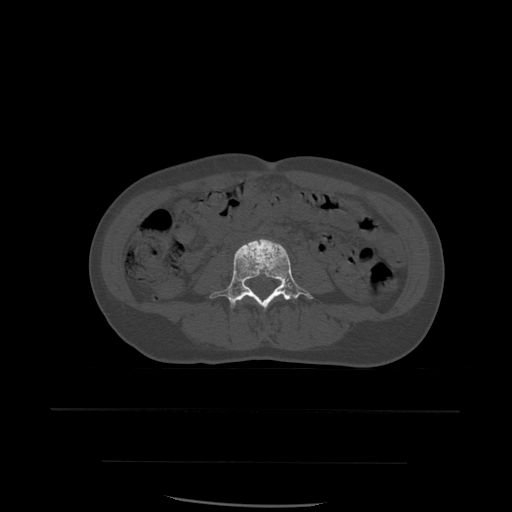
CT including the spine, one axial slice; bone window (W 1800 / L 400 HU); 1.25 mm slice thickness; 512 × 512 image matrix, field of view 392 × 392 mm. Patient age 48 years. Case-level facts recorded for this patient, not image findings: primary cancer: lung; vertebrae with lytic lesions (as recorded): T11.
Outlined on this slice (semi-automatically segmented with operator editing):
- L4 vertebra: bounding box [x1, y1, x2, y2] px = [210, 239, 313, 310]